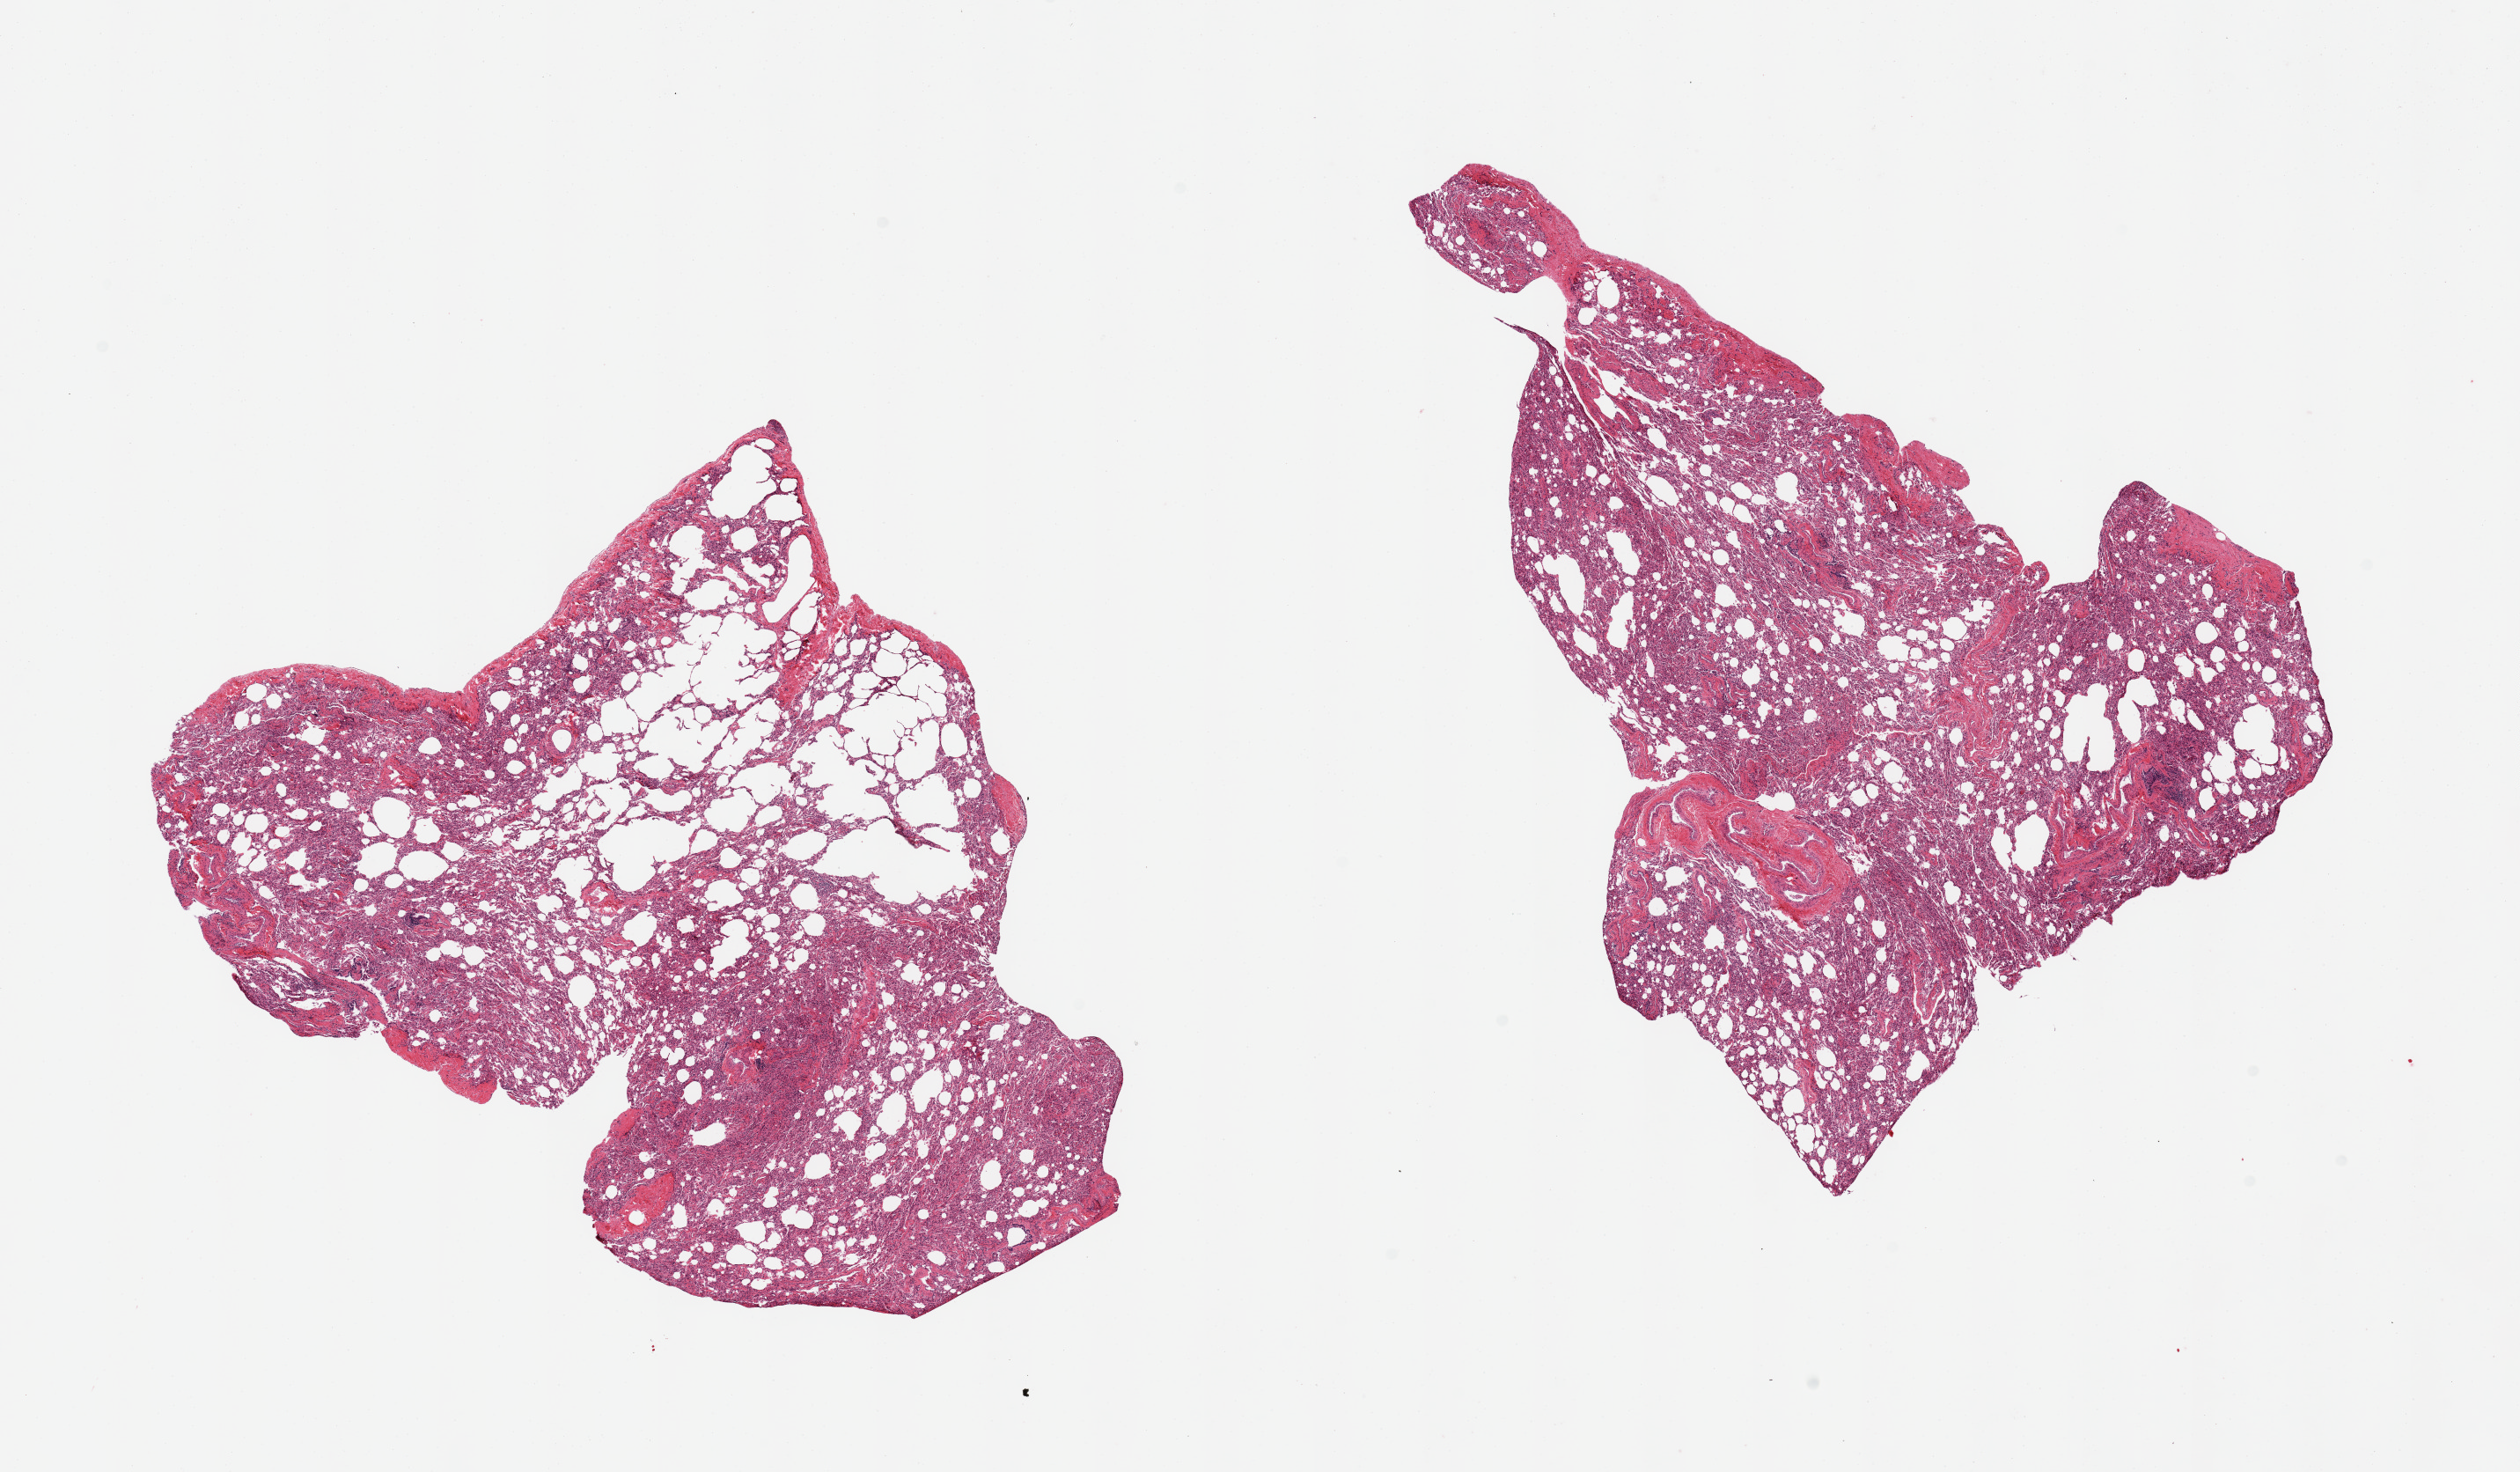
Digitized hematoxylin and eosin (H&E)-stained section — a low-resolution overview of the entire scanned area, about 22.6 x 13.2 mm (slide scanned at 20x). PAXgene-fixed, paraffin-embedded tissue. Target tissue: lung. Tissue donor sample.
• reviewer comment on this tissue sample: 2 pieces; emphysema